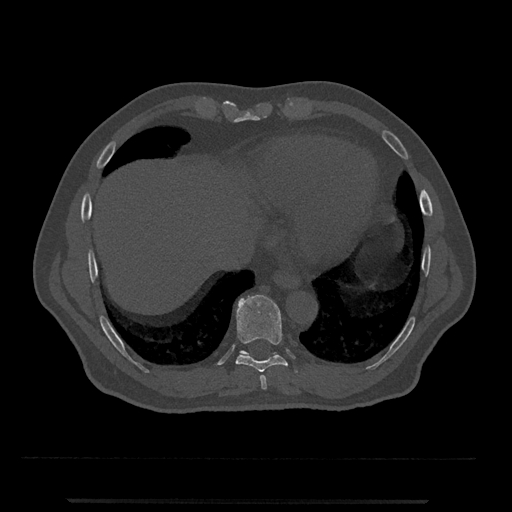
CT including the spine, one axial slice. Position 566 of 797 along the scan axis. Bone window (W 1800 / L 400 HU). 0.5 mm slice thickness. 512 × 512 image matrix, field of view 419 × 419 mm. Patient: male, 63 years. From the clinical record (not read from this slice): primary cancer: prostate.
Outlined on this slice (semi-automatically segmented with operator editing):
- T10 vertebra: bounding box <239,350,278,356> (left, top, right, bottom; pixels)
- T8 vertebra: <260,375,267,390>
- T9 vertebra: <235,294,288,372>